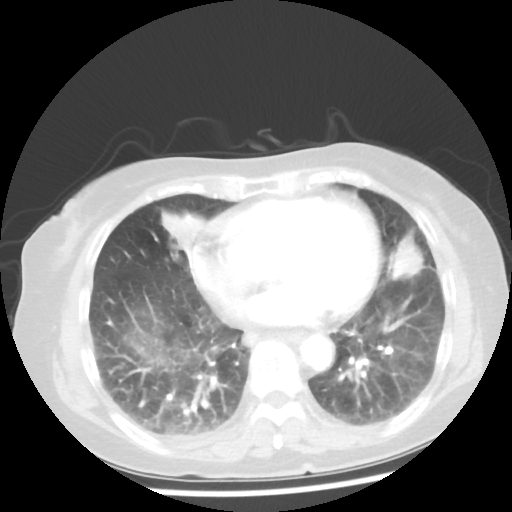
Chest CT, one axial slice. Position 17 of 50 along the scan axis. Reconstruction kernel STANDARD. Lung window (W 1500 / L -600 HU). 5 mm slice thickness. 512 × 512 image matrix. Female patient, age 77 years. Case-level facts recorded for this patient, not image findings: clinical TNM (as recorded): T2 N3 M1a.
Annotated regions visible in this slice (bounding box drawn by a radiologist):
- lung tumour (recorded histology: adenocarcinoma): bounding box [x1, y1, x2, y2] px = [387, 224, 430, 284]